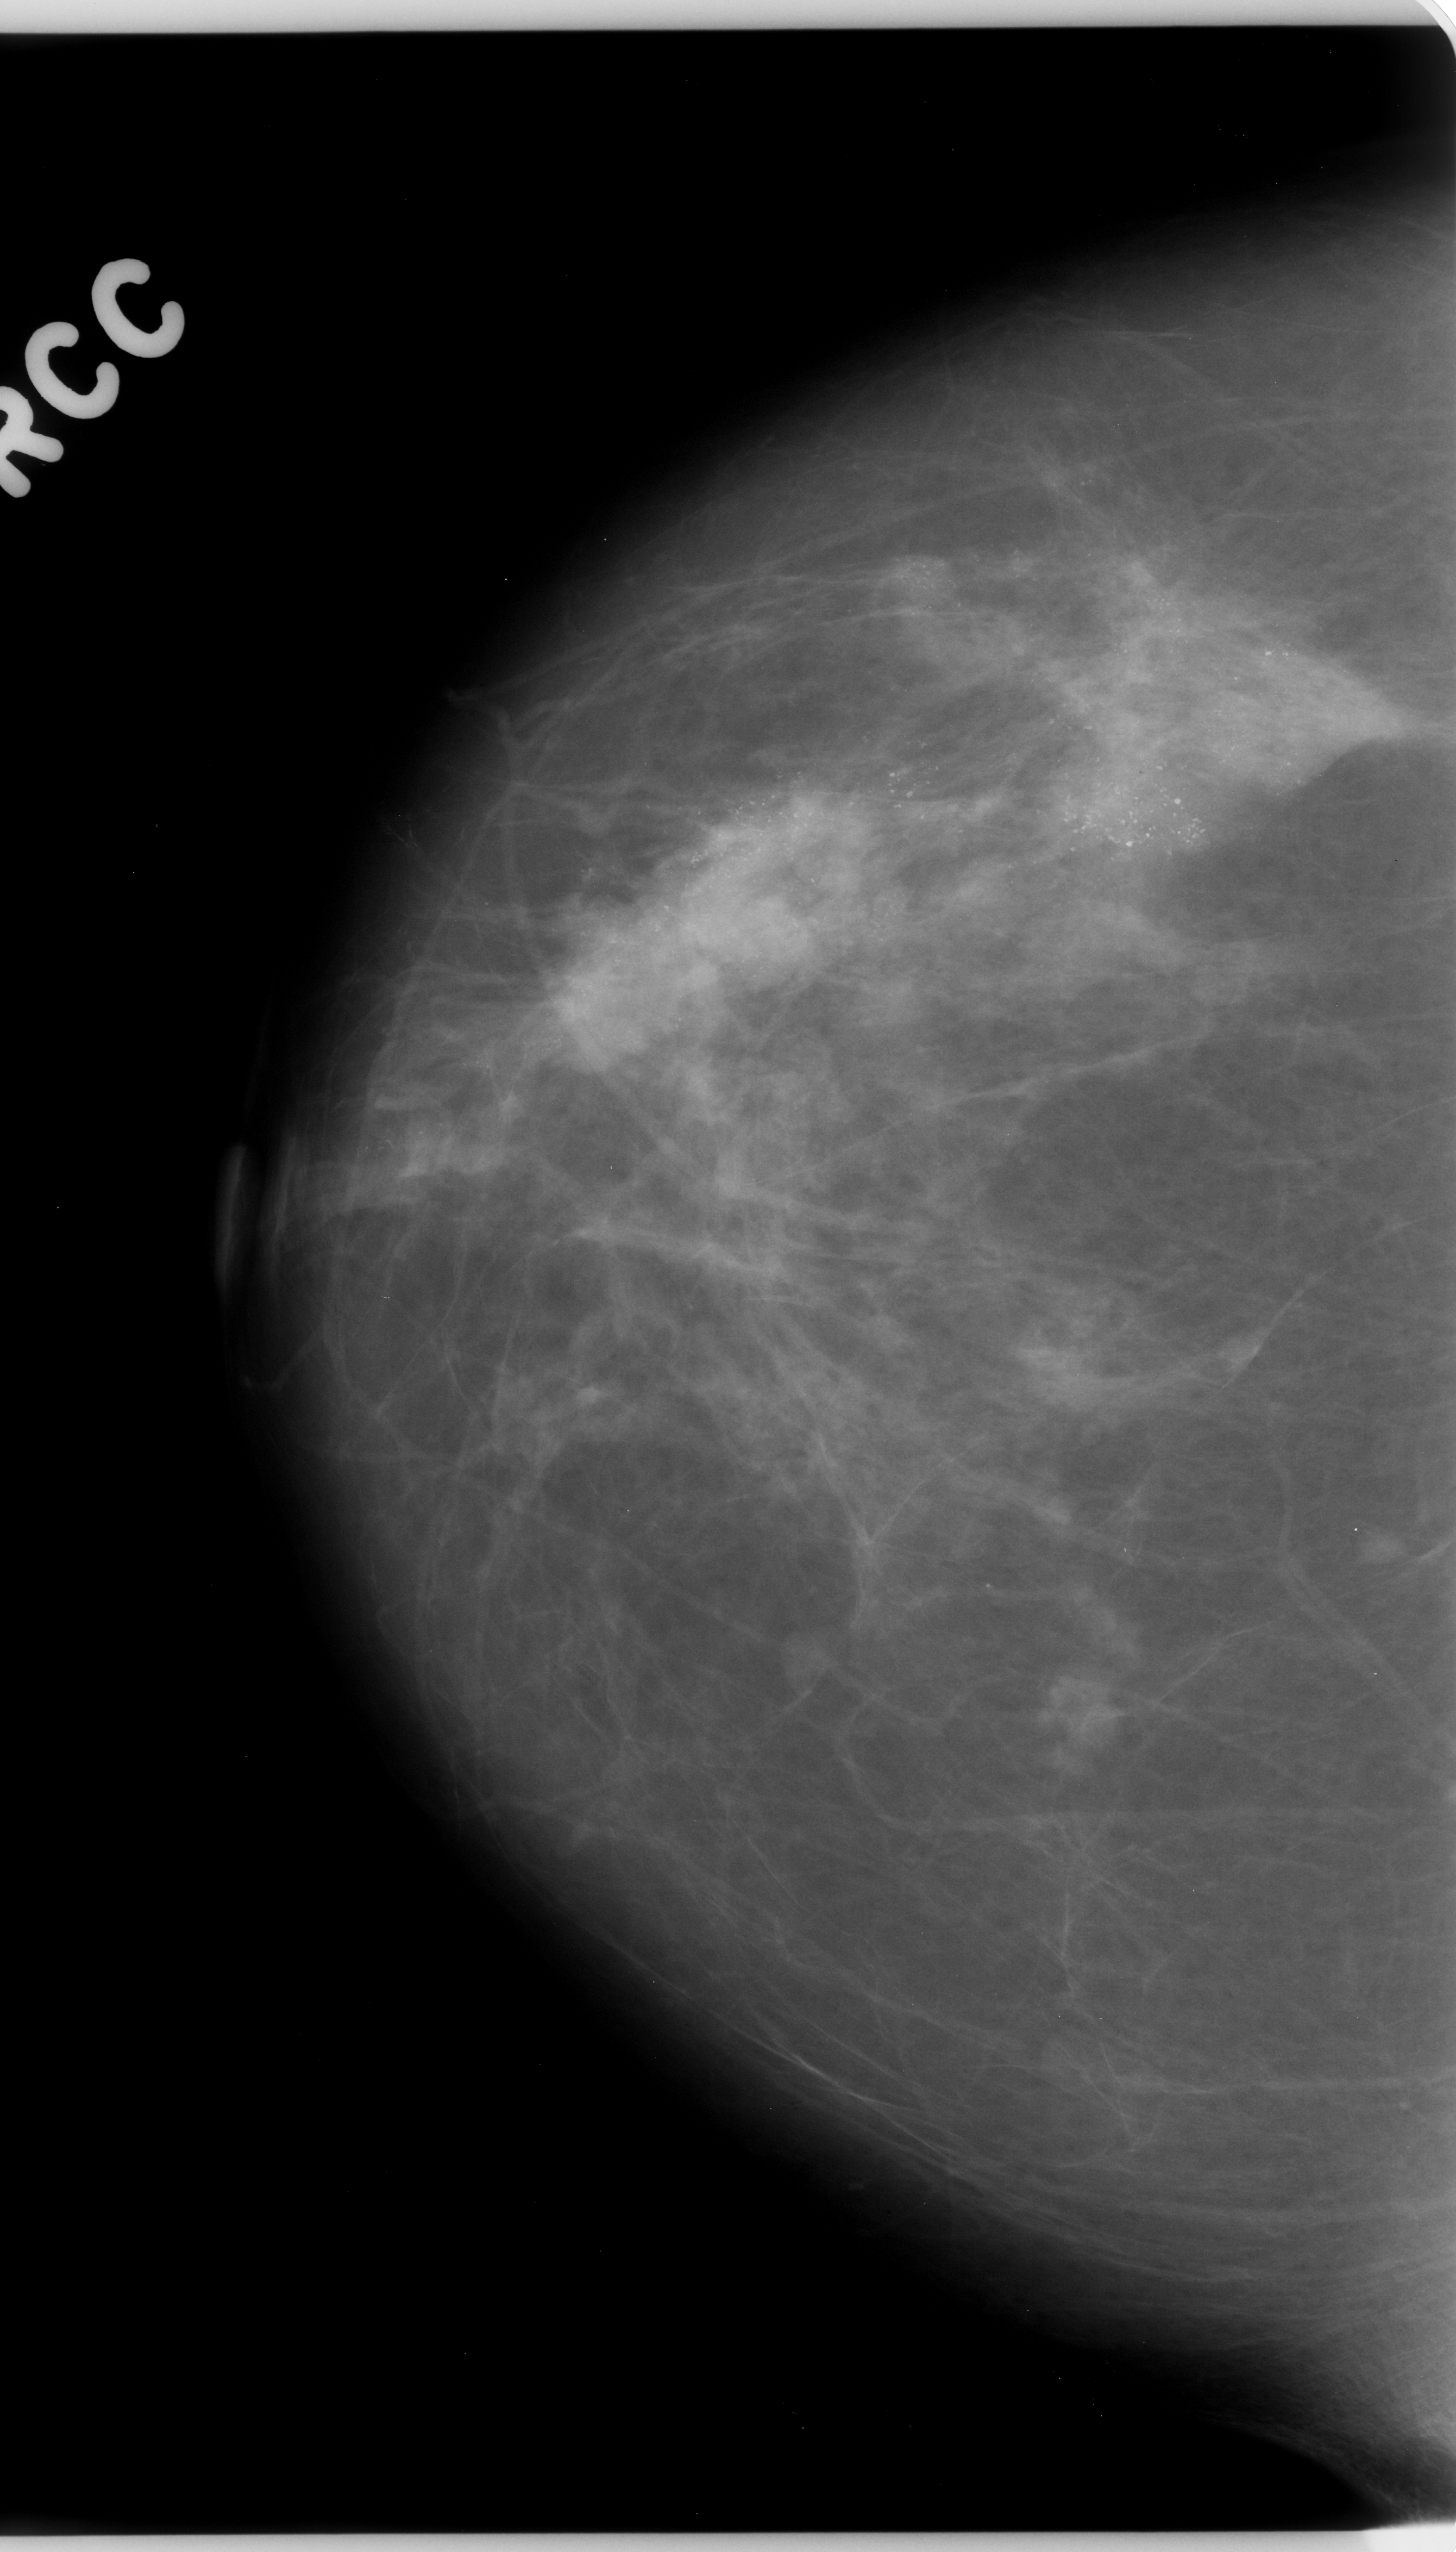
Mammogram (digitized film); right breast; craniocaudal (CC) view; BI-RADS breast density category 2 (scale 1–4); 1456 × 2552 image matrix.
Expert-marked regions of interest on this film, with their recorded descriptors:
- calcifications, morphology pleomorphic, distribution regional; BI-RADS assessment category 5; subtlety rating 5 on a 1 (subtle) to 5 (obvious) scale; pathology (as recorded): malignant: box from (x=391, y=491) to (x=1427, y=1131) px